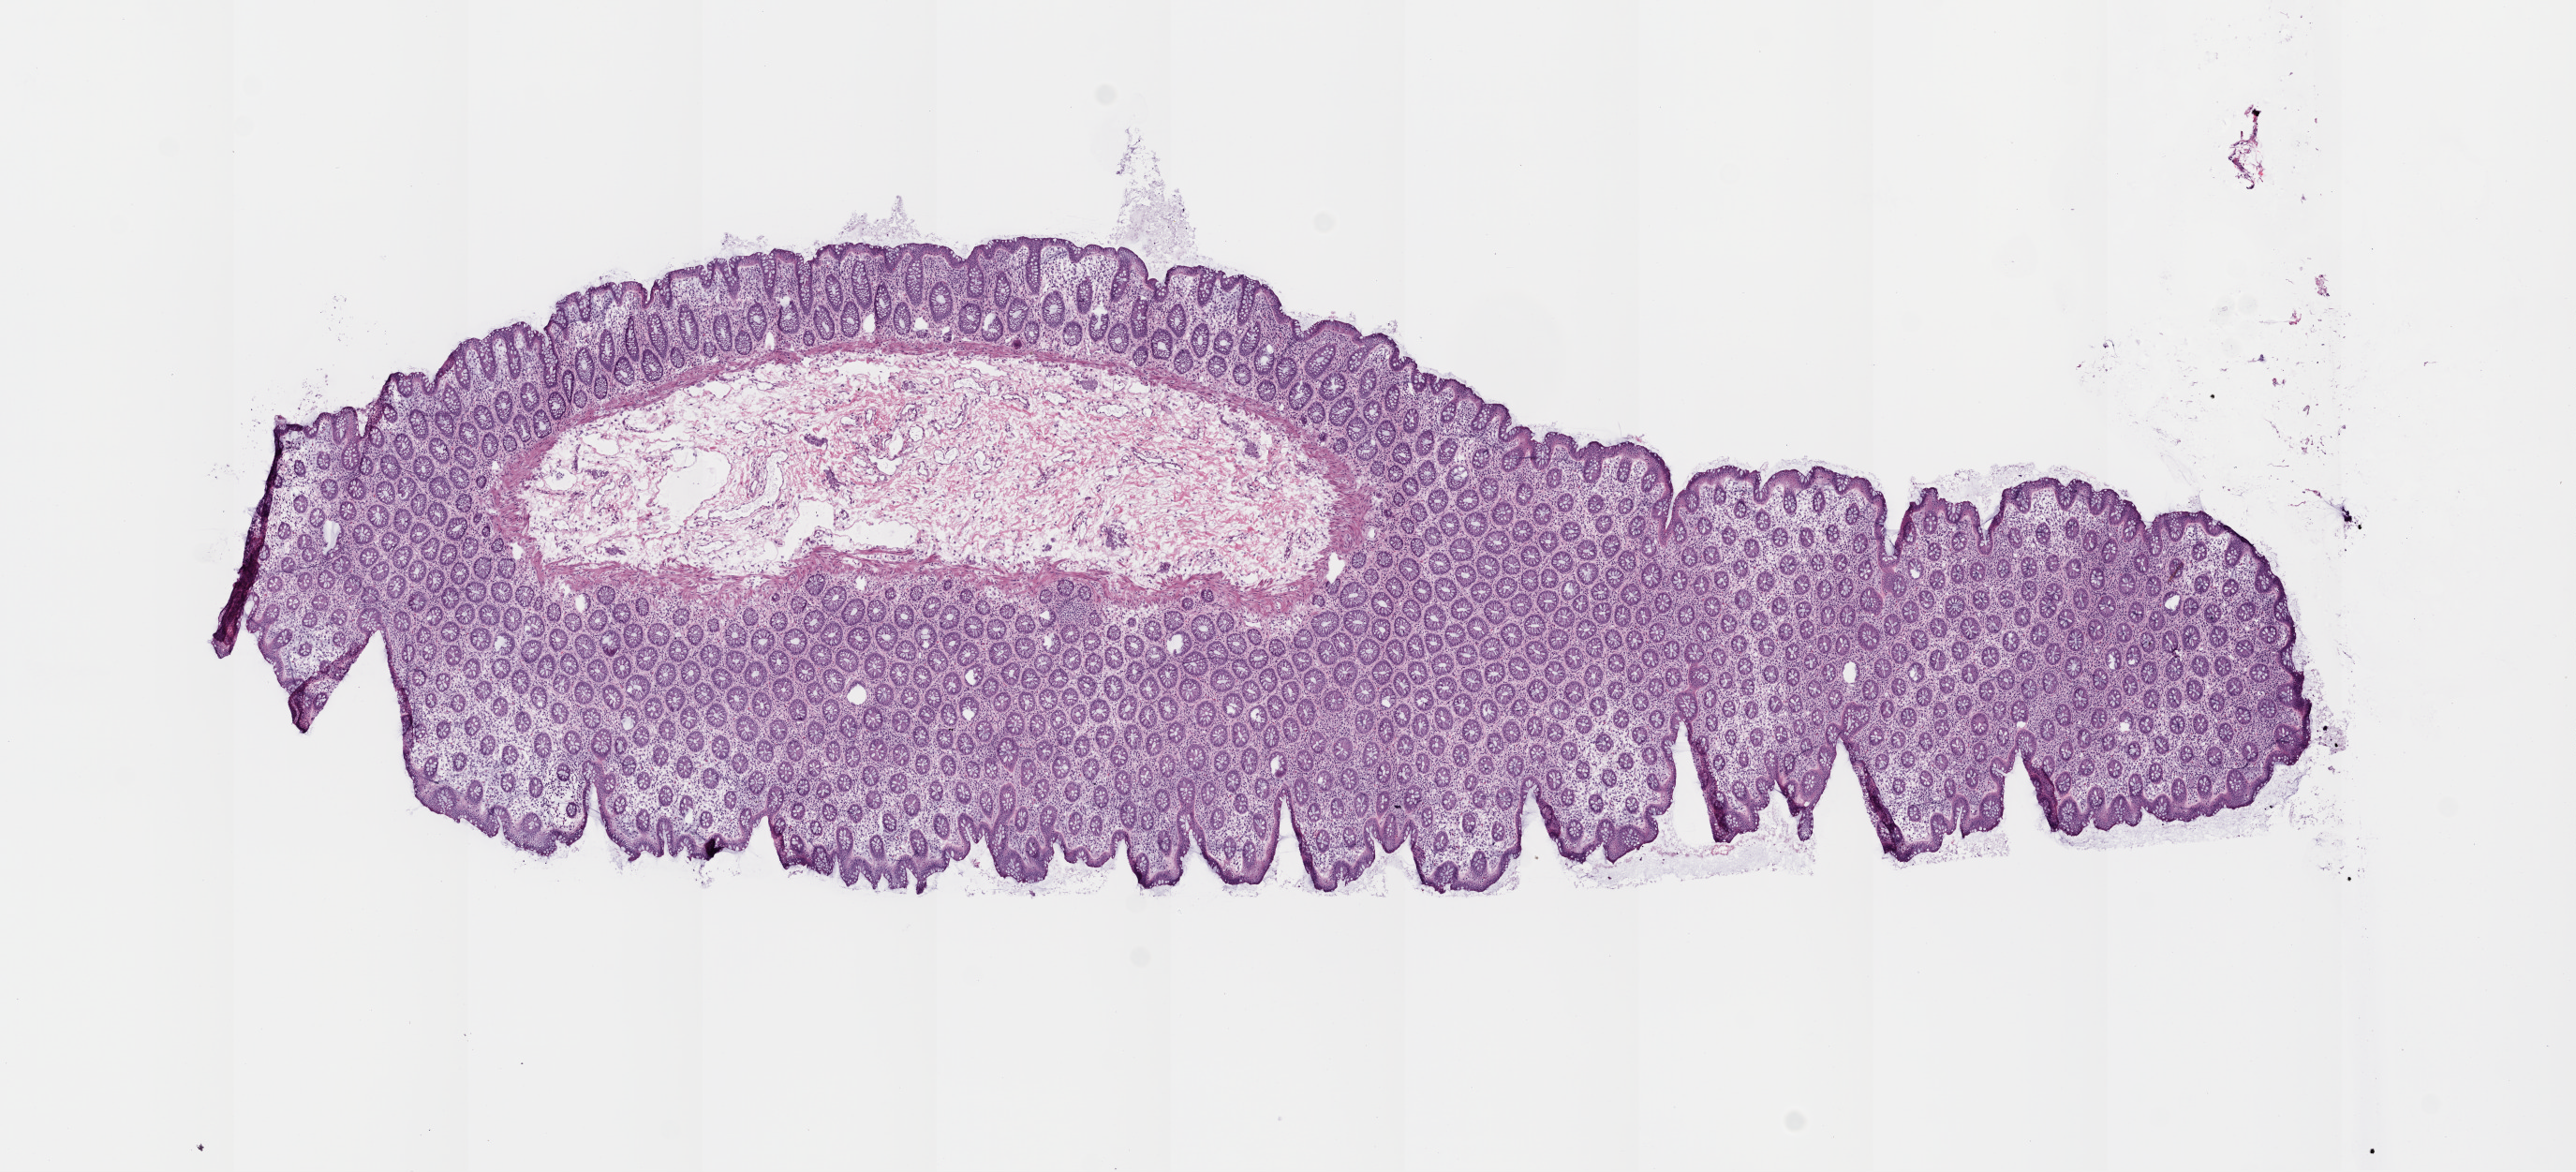
Digitized Hematoxylin and eosin (H&E) stained tissue section (whole slide), low-resolution overview of the scanned area, about 11.0 x 5.0 mm (from a 20x scan). Frozen section from the top of the tissue portion. Colon, solid tissue normal (non-tumour tissue) sample. Female patient; age at initial diagnosis 48 years.
This section: solid tissue normal (non-tumour) sample from the same patient. Patient diagnosis: Adenocarcinoma, NOS.